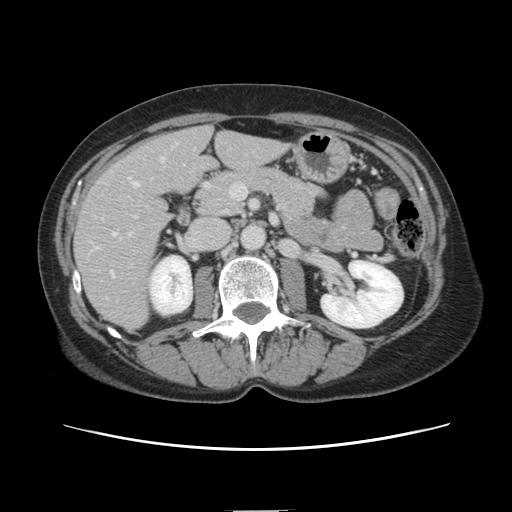
Contrast-enhanced abdominal CT, one axial slice; slice 56 of 141 in the series (ordered by position); 120 kVp; soft-tissue window (W 400 / L 40 HU); 512 × 512 image matrix, field of view 350 × 350 mm. Female patient, age 63 years. Case-level facts recorded for this patient, not image findings: diagnosis: colorectal cancer liver metastases, imaged before liver resection; multiple liver metastases: yes; largest metastasis: 3.2 cm; disease in both lobes: yes.
Outlined on this slice (manually delineated by an expert):
- hepatic veins: box from (x=111, y=159) to (x=163, y=273) px
- liver: (x=76, y=126)–(x=285, y=330)
- planned liver remnant (the part of the liver to remain after resection): (x=177, y=127)–(x=285, y=184)